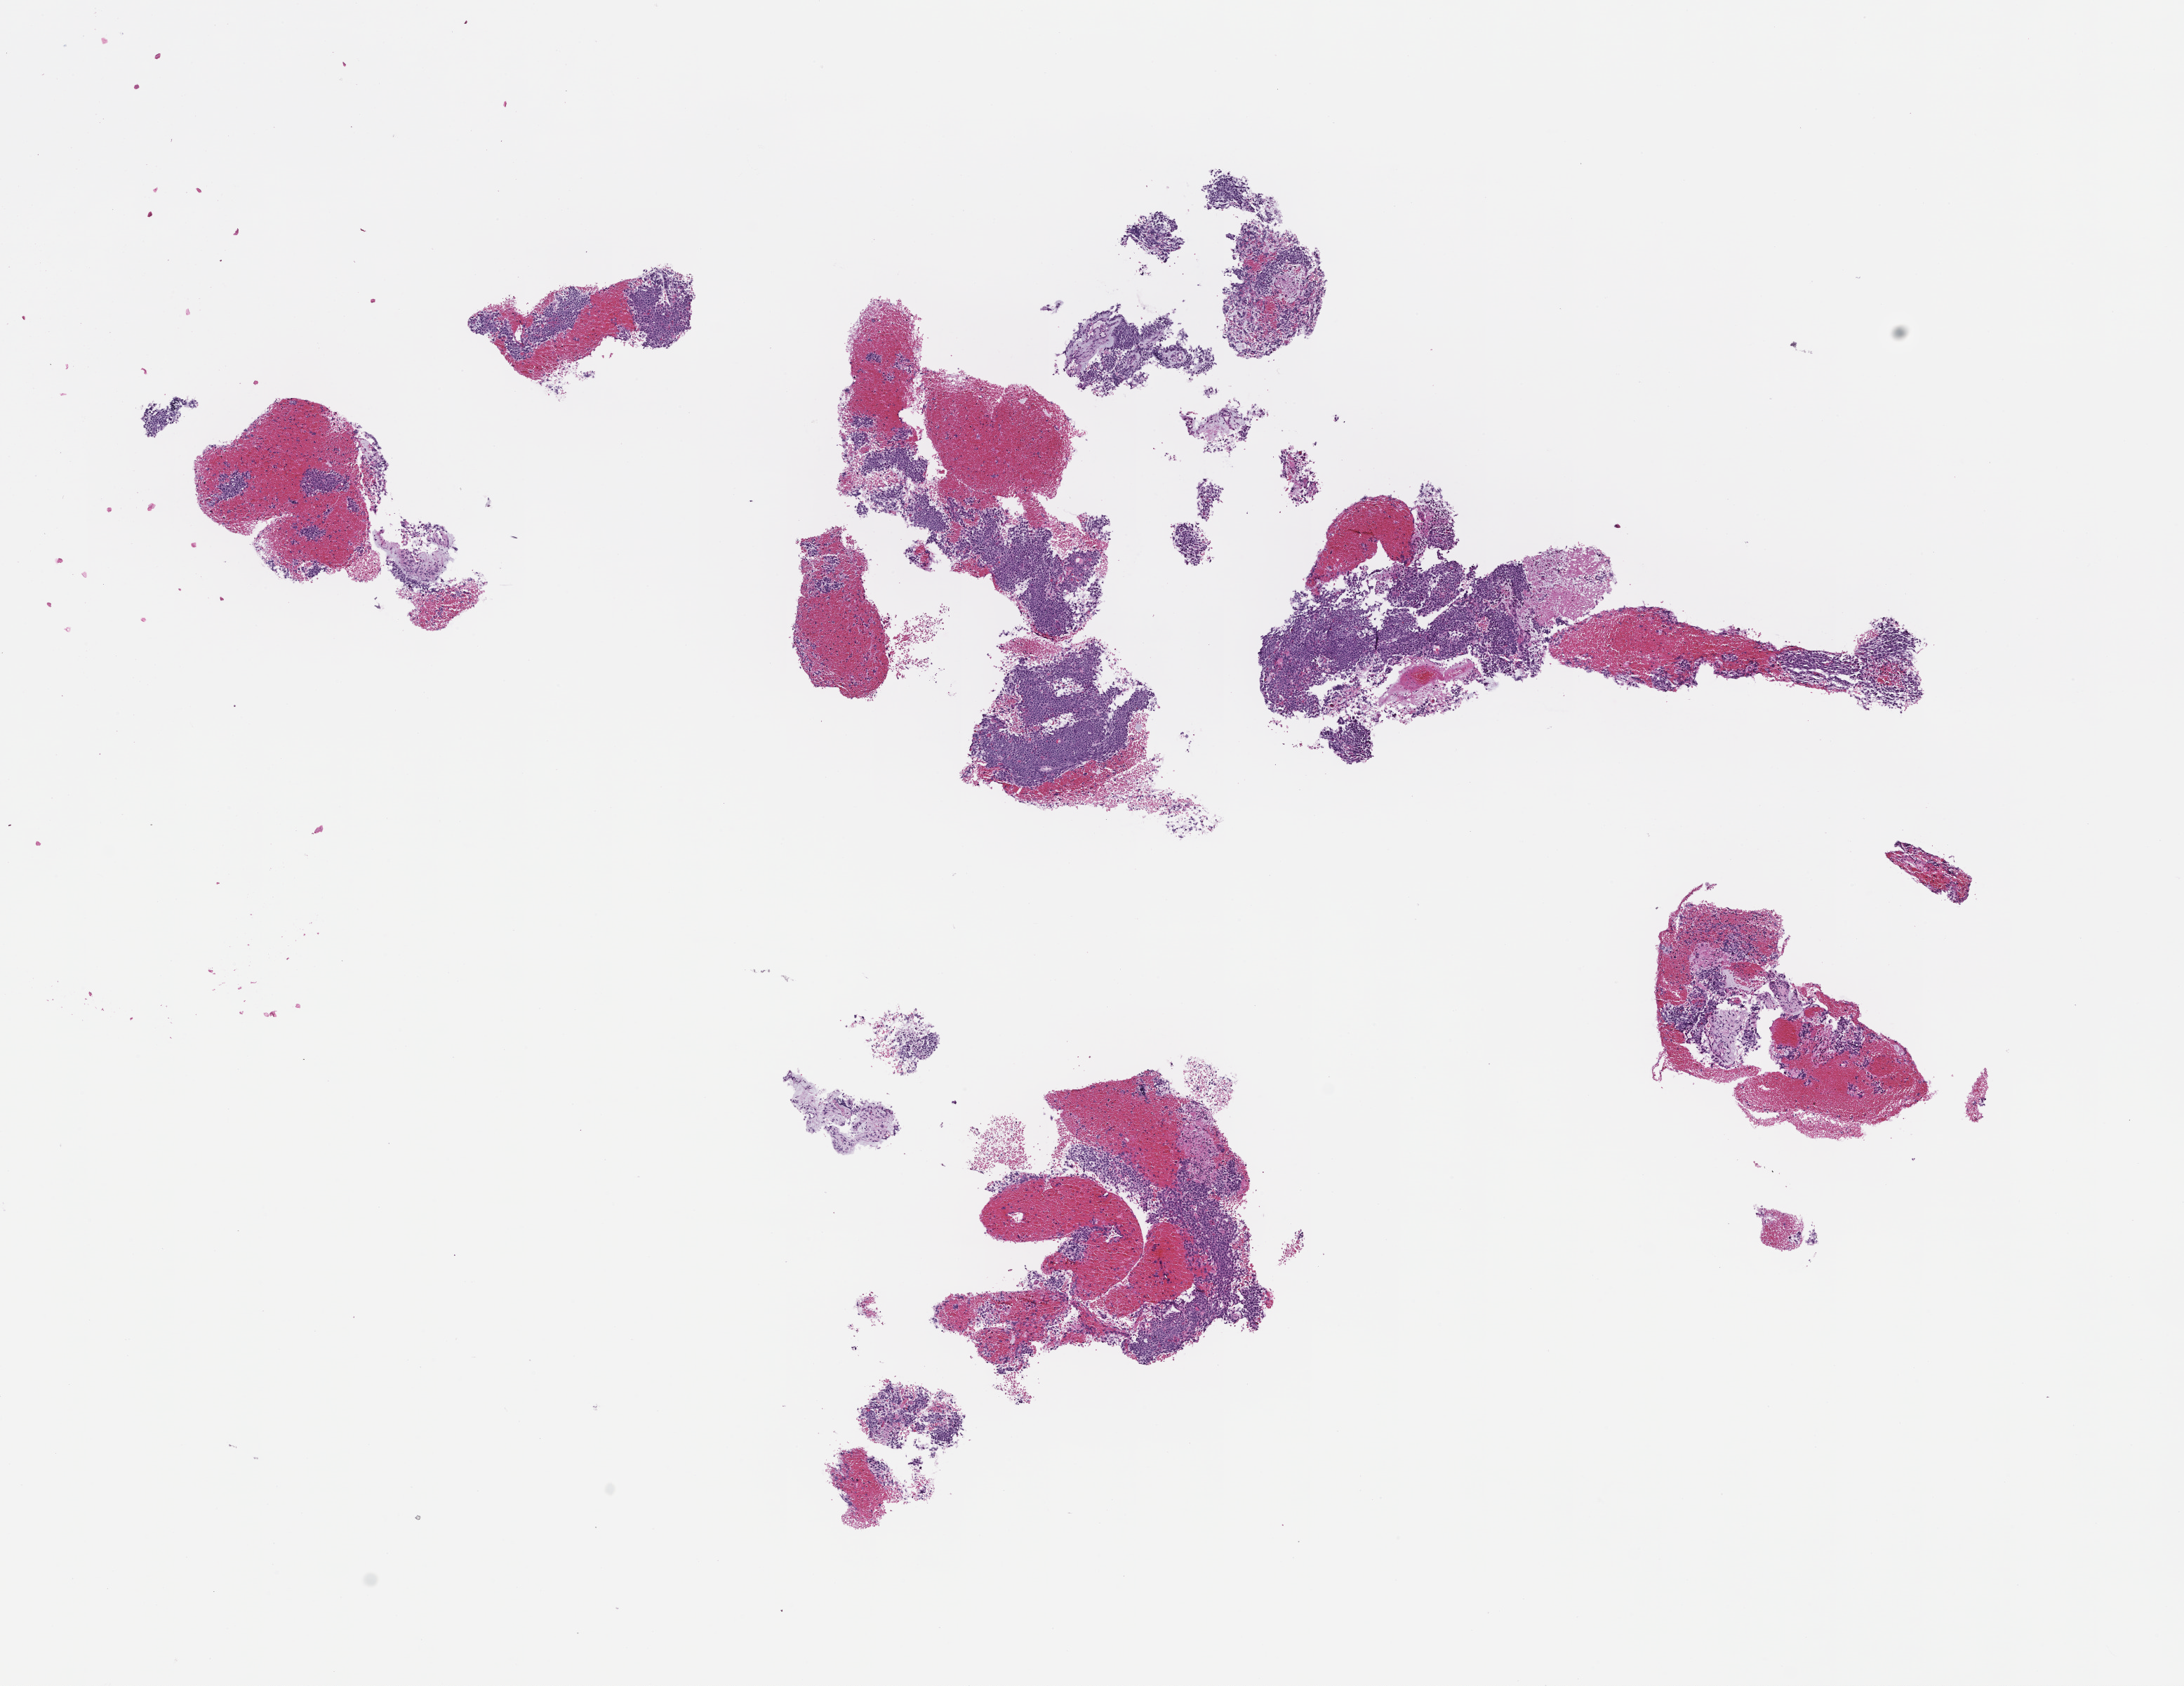
Whole-slide image, haematoxylin and eosin stain — low-resolution overview of the scanned area, about 12.6 x 9.7 mm. Formalin-fixed paraffin-embedded section. Specimen time point: collected at disease progression. Patient: male.
This section: metastasis (sampled organ not recorded). Primary diagnosis of the patient: Prostate Carcinoma.